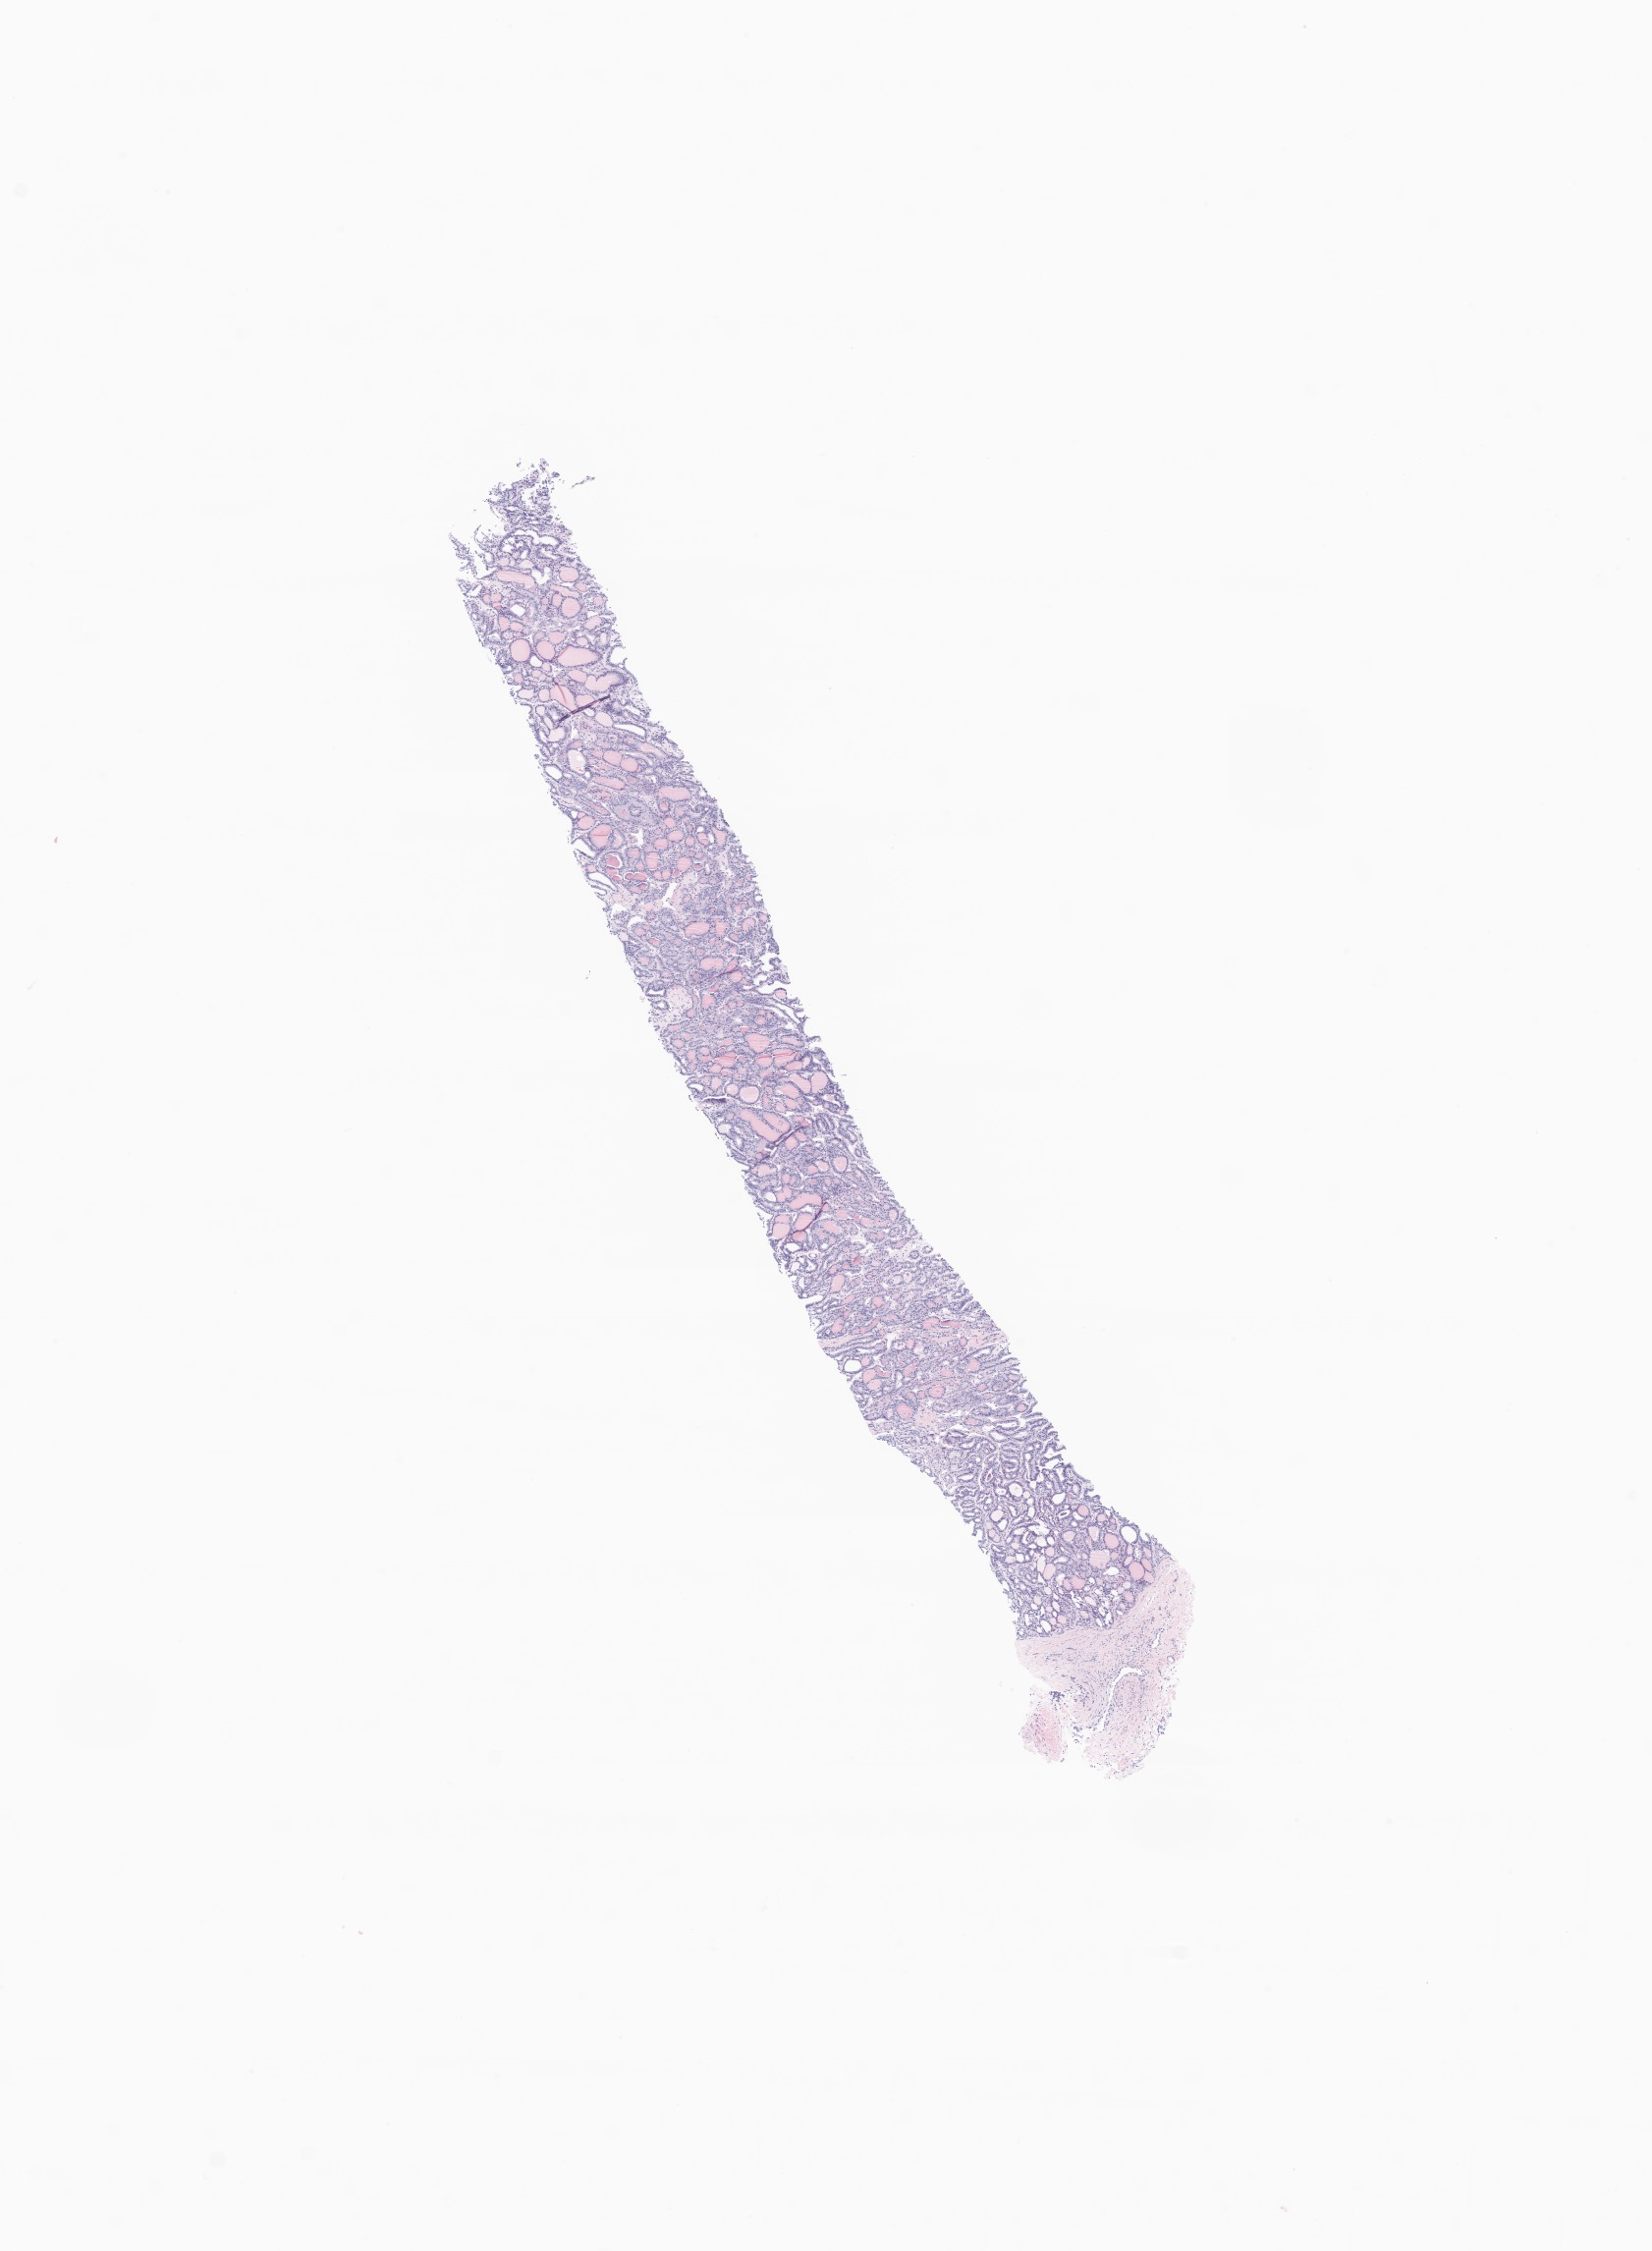
H&E whole-slide image of tumor tissue from the thyroid — low-resolution overview of the scanned area, about 7.1 x 9.7 mm; formalin-fixed paraffin-embedded section. Patient: female, age 43 months (3 years 7 months).
• recorded diagnosis: Papillary carcinoma, NOS